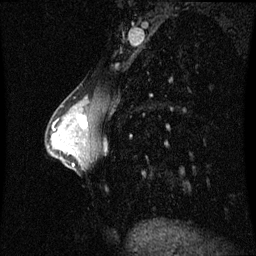
Breast MRI (dynamic contrast-enhanced), one sagittal slice; slice 26 of 60 in the series (ordered by position); dynamic contrast-enhanced series, image 2 of 3 at this slice position (ordered by acquisition); 1.5 T; TE 4.2 ms, TR 8.9 ms; 2 mm slice thickness; 256 × 256 image matrix. Patient: female, 33 years. Case-level facts recorded for this patient, not image findings: setting: breast cancer imaged before/during neoadjuvant chemotherapy; receptor status: HER2-positive.
Annotated regions visible in this slice (semi-automatic segmentation, software-assisted and operator-edited):
- analysis volume of interest (the breast-tissue region the enhancement analysis was run in; not a lesion): box from (x=66, y=102) to (x=94, y=141) px
- tumour enhancement mask (voxels above the 70 % enhancement threshold inside the analysis volume of interest): (x=78, y=116)–(x=89, y=129)